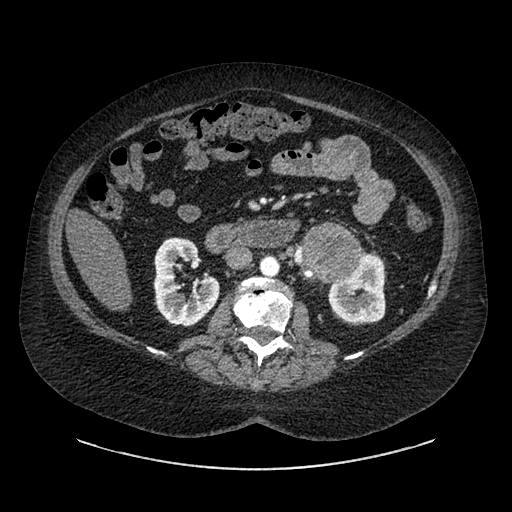
Contrast-enhanced abdominal CT, one axial slice; position 501 of 769 along the scan axis; reconstruction kernel SOFT; 120 kVp; intravenous contrast given; soft-tissue window (W 400 / L 40 HU); 0.62 mm slice thickness; 512 × 512 image matrix, field of view 460 × 460 mm. Patient: female, 61 years. From the clinical record (not read from this slice): diagnosis: adrenocortical carcinoma; tumour side: left adrenal; tumour size at pathology: 13 cm; Ki-67 index: 79 %; stage (as recorded): 2.
Structures marked on this image (semi-automatically segmented with operator editing):
- mass: bounding box <306,226,360,280> (left, top, right, bottom; pixels)